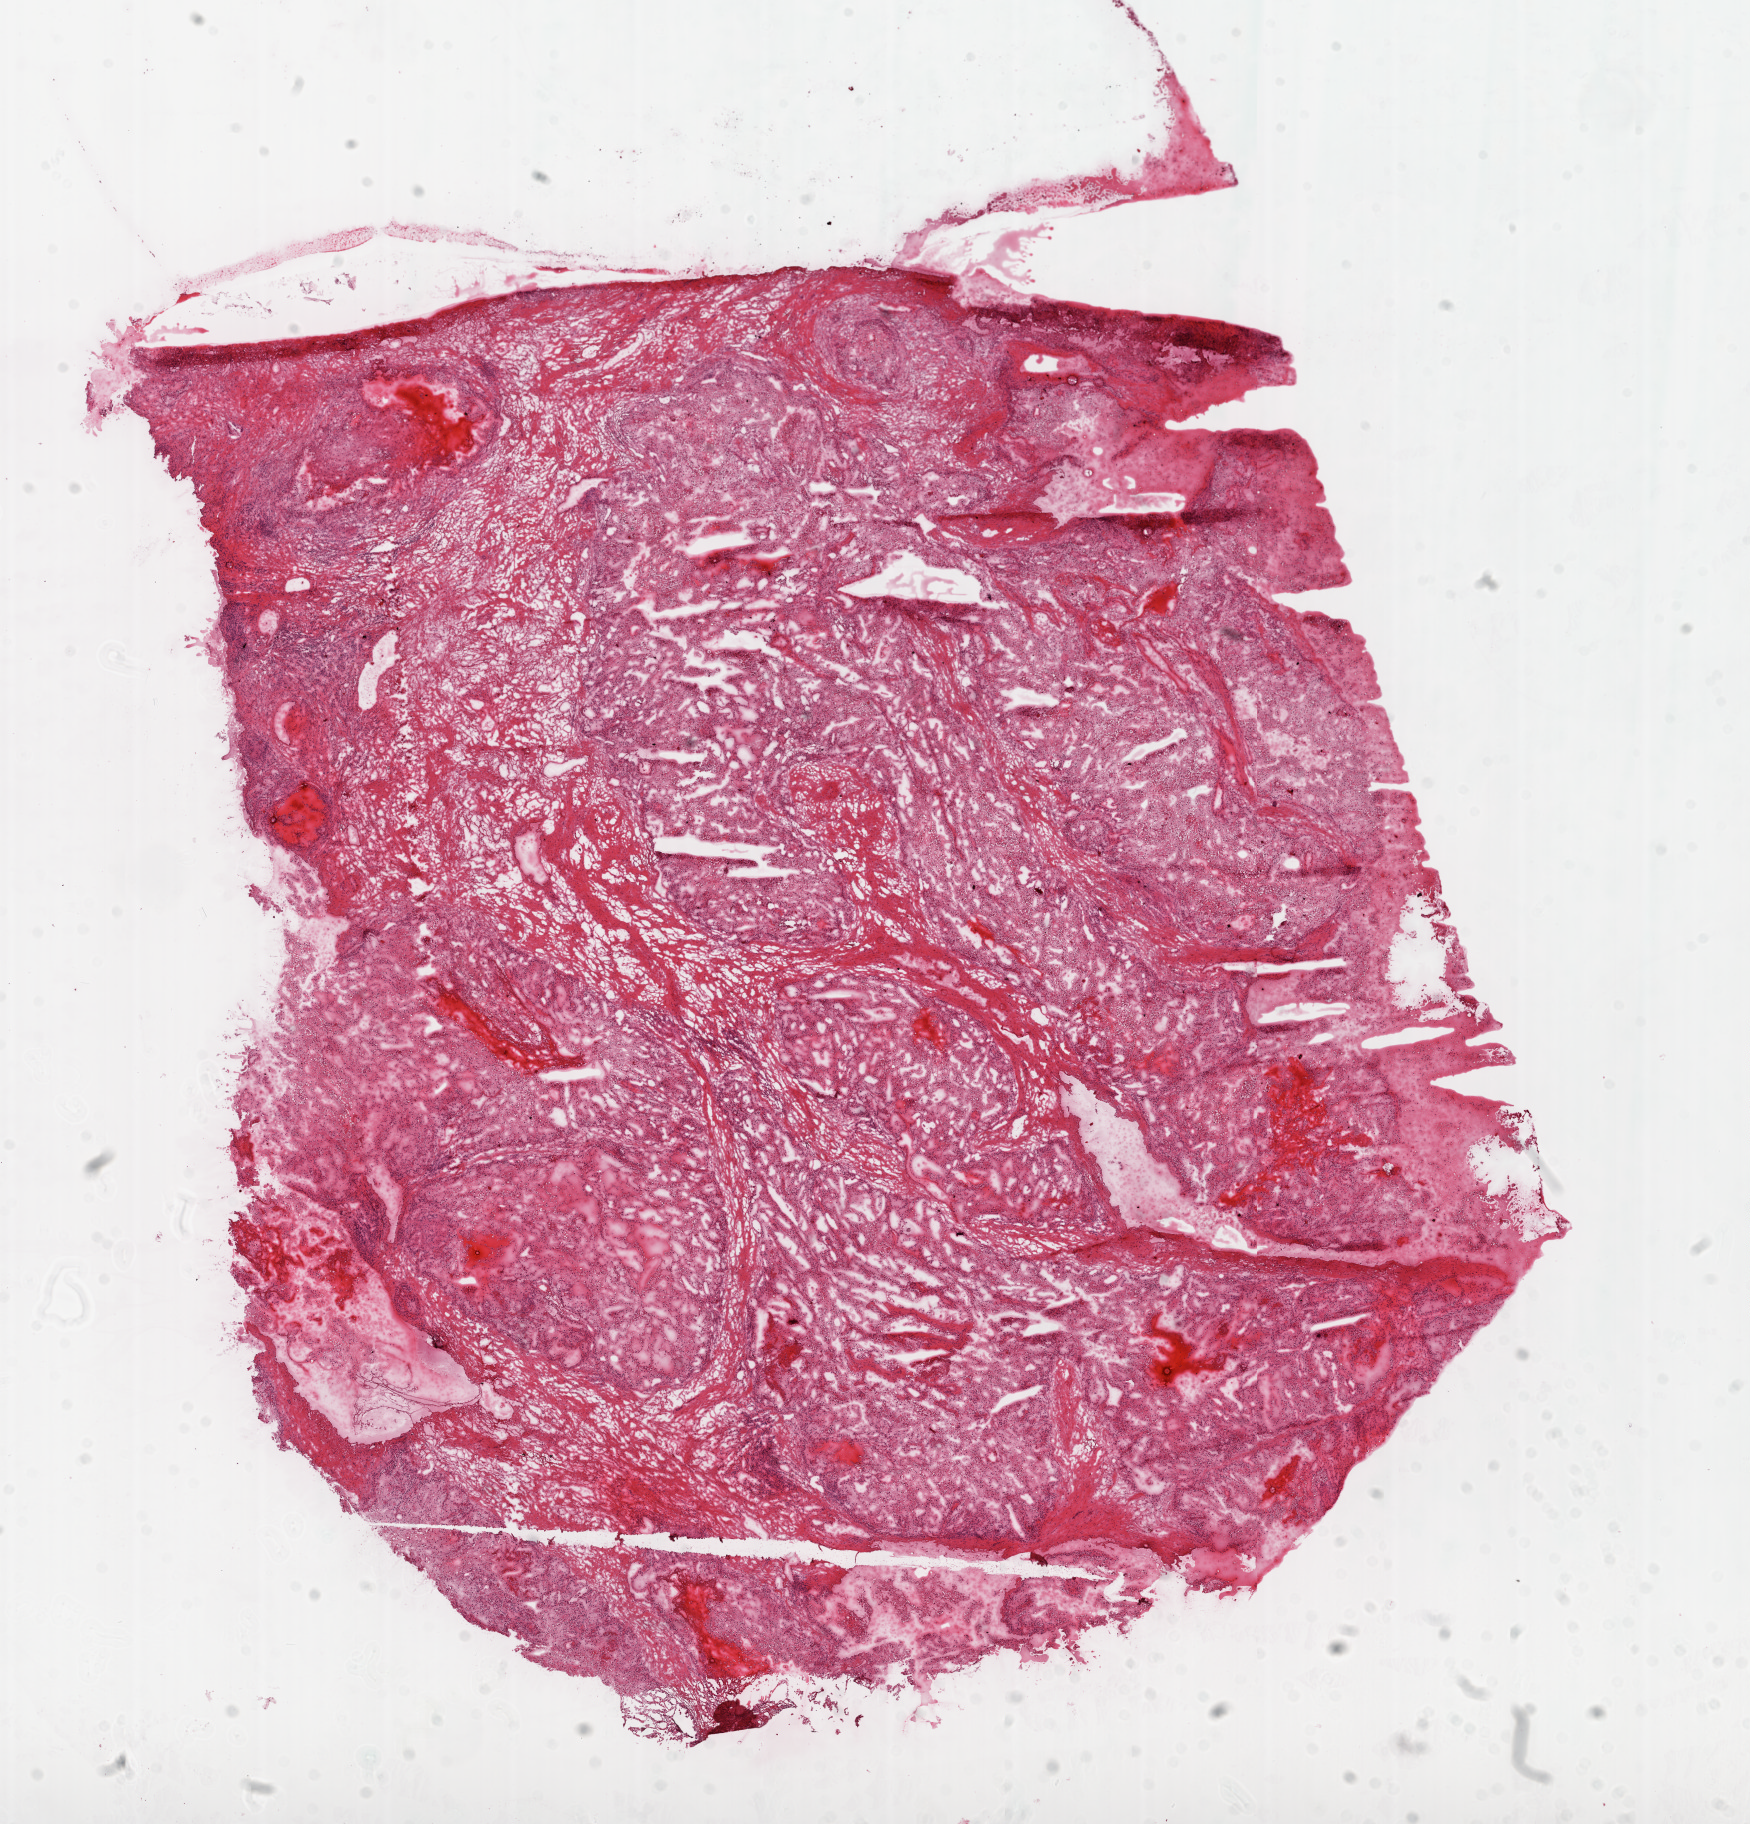
H&E whole-slide image — whole scanned area (about 14.0 x 14.6 mm) shown as a low-resolution overview, frozen section from the top of the tissue portion, primary tumour sample from the kidney. Patient: male, age at initial diagnosis 40 years. Histologic grade: G3 (poorly differentiated). Slide review estimates, as recorded: tumour cells 75%, tumour nuclei 80%, normal cells 0%, stromal cells 25%, necrosis 0%.
* diagnosis: Clear cell adenocarcinoma, NOS
* lymph nodes positive (case pathology): 0 of 5 examined
* AJCC pathologic stage: III